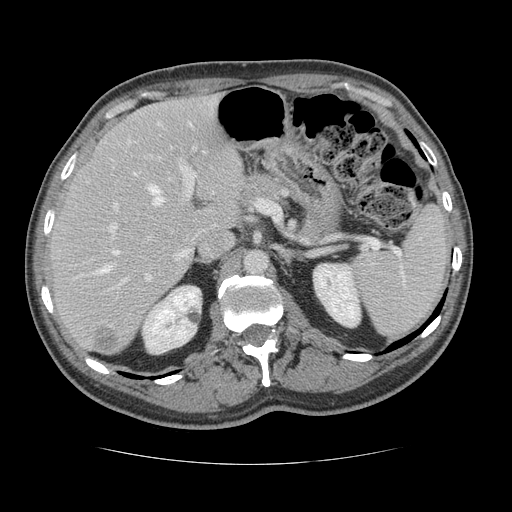
Contrast-enhanced abdominal CT, one axial slice. Position 83 of 134 along the scan axis. Reconstruction kernel STANDARD. 120 kVp. Intravenous contrast given. Soft-tissue window (W 400 / L 40 HU). 2.5 mm slice thickness. 512 × 512 image matrix. Male patient, age 68 years. Case-level facts recorded for this patient, not image findings: diagnosis: colorectal cancer liver metastases, imaged before liver resection; multiple liver metastases: yes; largest metastasis: 2.2 cm; disease in both lobes: no.
Structures marked on this image (manually delineated by an expert):
- hepatic veins: bounding box <80,123,213,275> (left, top, right, bottom; pixels)
- liver: <51,93,247,354>
- planned liver remnant (the part of the liver to remain after resection): <51,93,246,337>
- portal vein (with intrahepatic branches): <110,122,197,283>
- liver metastasis: <95,329,123,353>